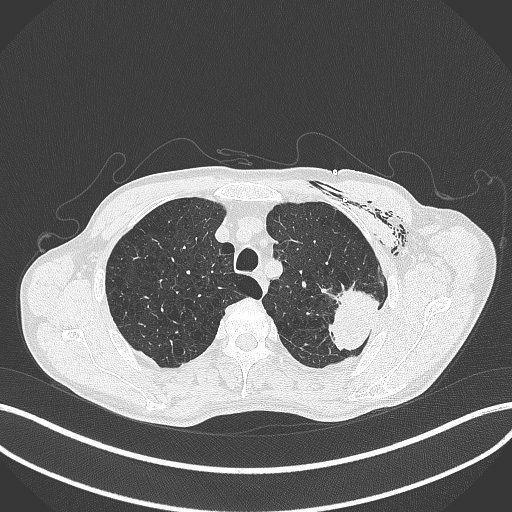
Chest CT, one axial slice; slice 332 of 457 in the series (ordered by position); reconstruction kernel B70f; 120 kVp; lung window (W 1500 / L -600 HU); 1 mm slice thickness; 512 × 512 image matrix, field of view 400 × 400 mm. Patient: male, 58 years. From the clinical record (not read from this slice): clinical TNM (as recorded): T3 N0 M0.
Annotated regions visible in this slice (rectangle marked by the reading radiologist):
- lung tumour (recorded histology: adenocarcinoma): bounding box (x1, y1, x2, y2) in pixels: (325, 280, 384, 354)